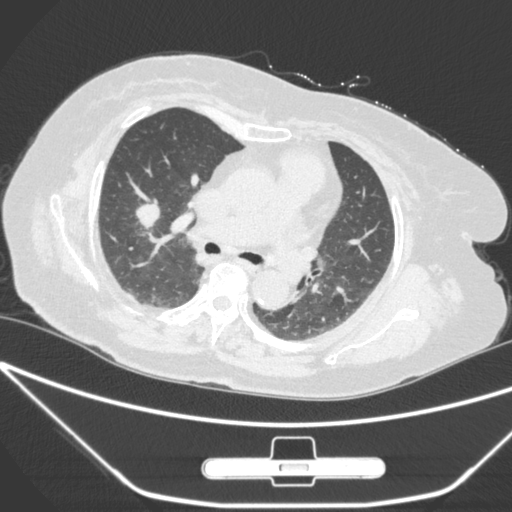
Chest CT, one axial slice; position 161 of 245 along the scan axis; 120 kVp; lung window (W 1500 / L -600 HU); 1 mm slice thickness; 512 × 512 image matrix, field of view 365 × 365 mm. Female patient, age 65 years. From the clinical record (not read from this slice): clinical TNM (as recorded): T1c N0 M0.
Outlined on this slice (rectangle marked by the reading radiologist):
- lung tumour (recorded histology: adenocarcinoma): bounding box (x1, y1, x2, y2) in pixels: (131, 189, 168, 233)